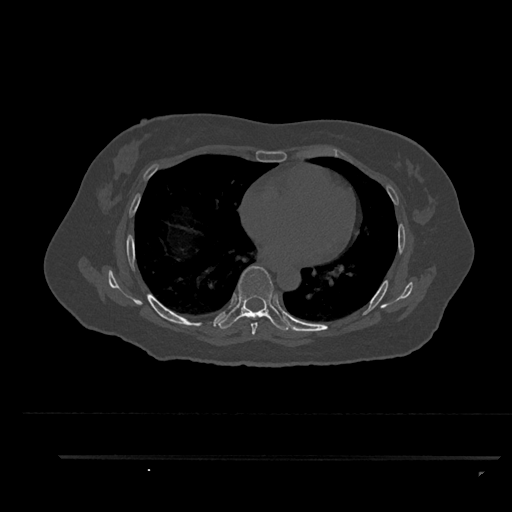
CT including the spine, one axial slice; slice 522 of 797 in the series (ordered by position); 120 kVp; bone window (W 1800 / L 400 HU); 0.5 mm slice thickness; 512 × 512 image matrix, field of view 408 × 408 mm. Female patient, age 44 years. From the clinical record (not read from this slice): primary cancer: renal; vertebrae with lytic lesions (as recorded): L1.
Annotated regions visible in this slice (semi-automatic segmentation, software-assisted and operator-edited):
- T6 vertebra: bounding box (x1, y1, x2, y2) in pixels: (249, 317, 258, 335)
- T7 vertebra: (218, 266, 291, 331)